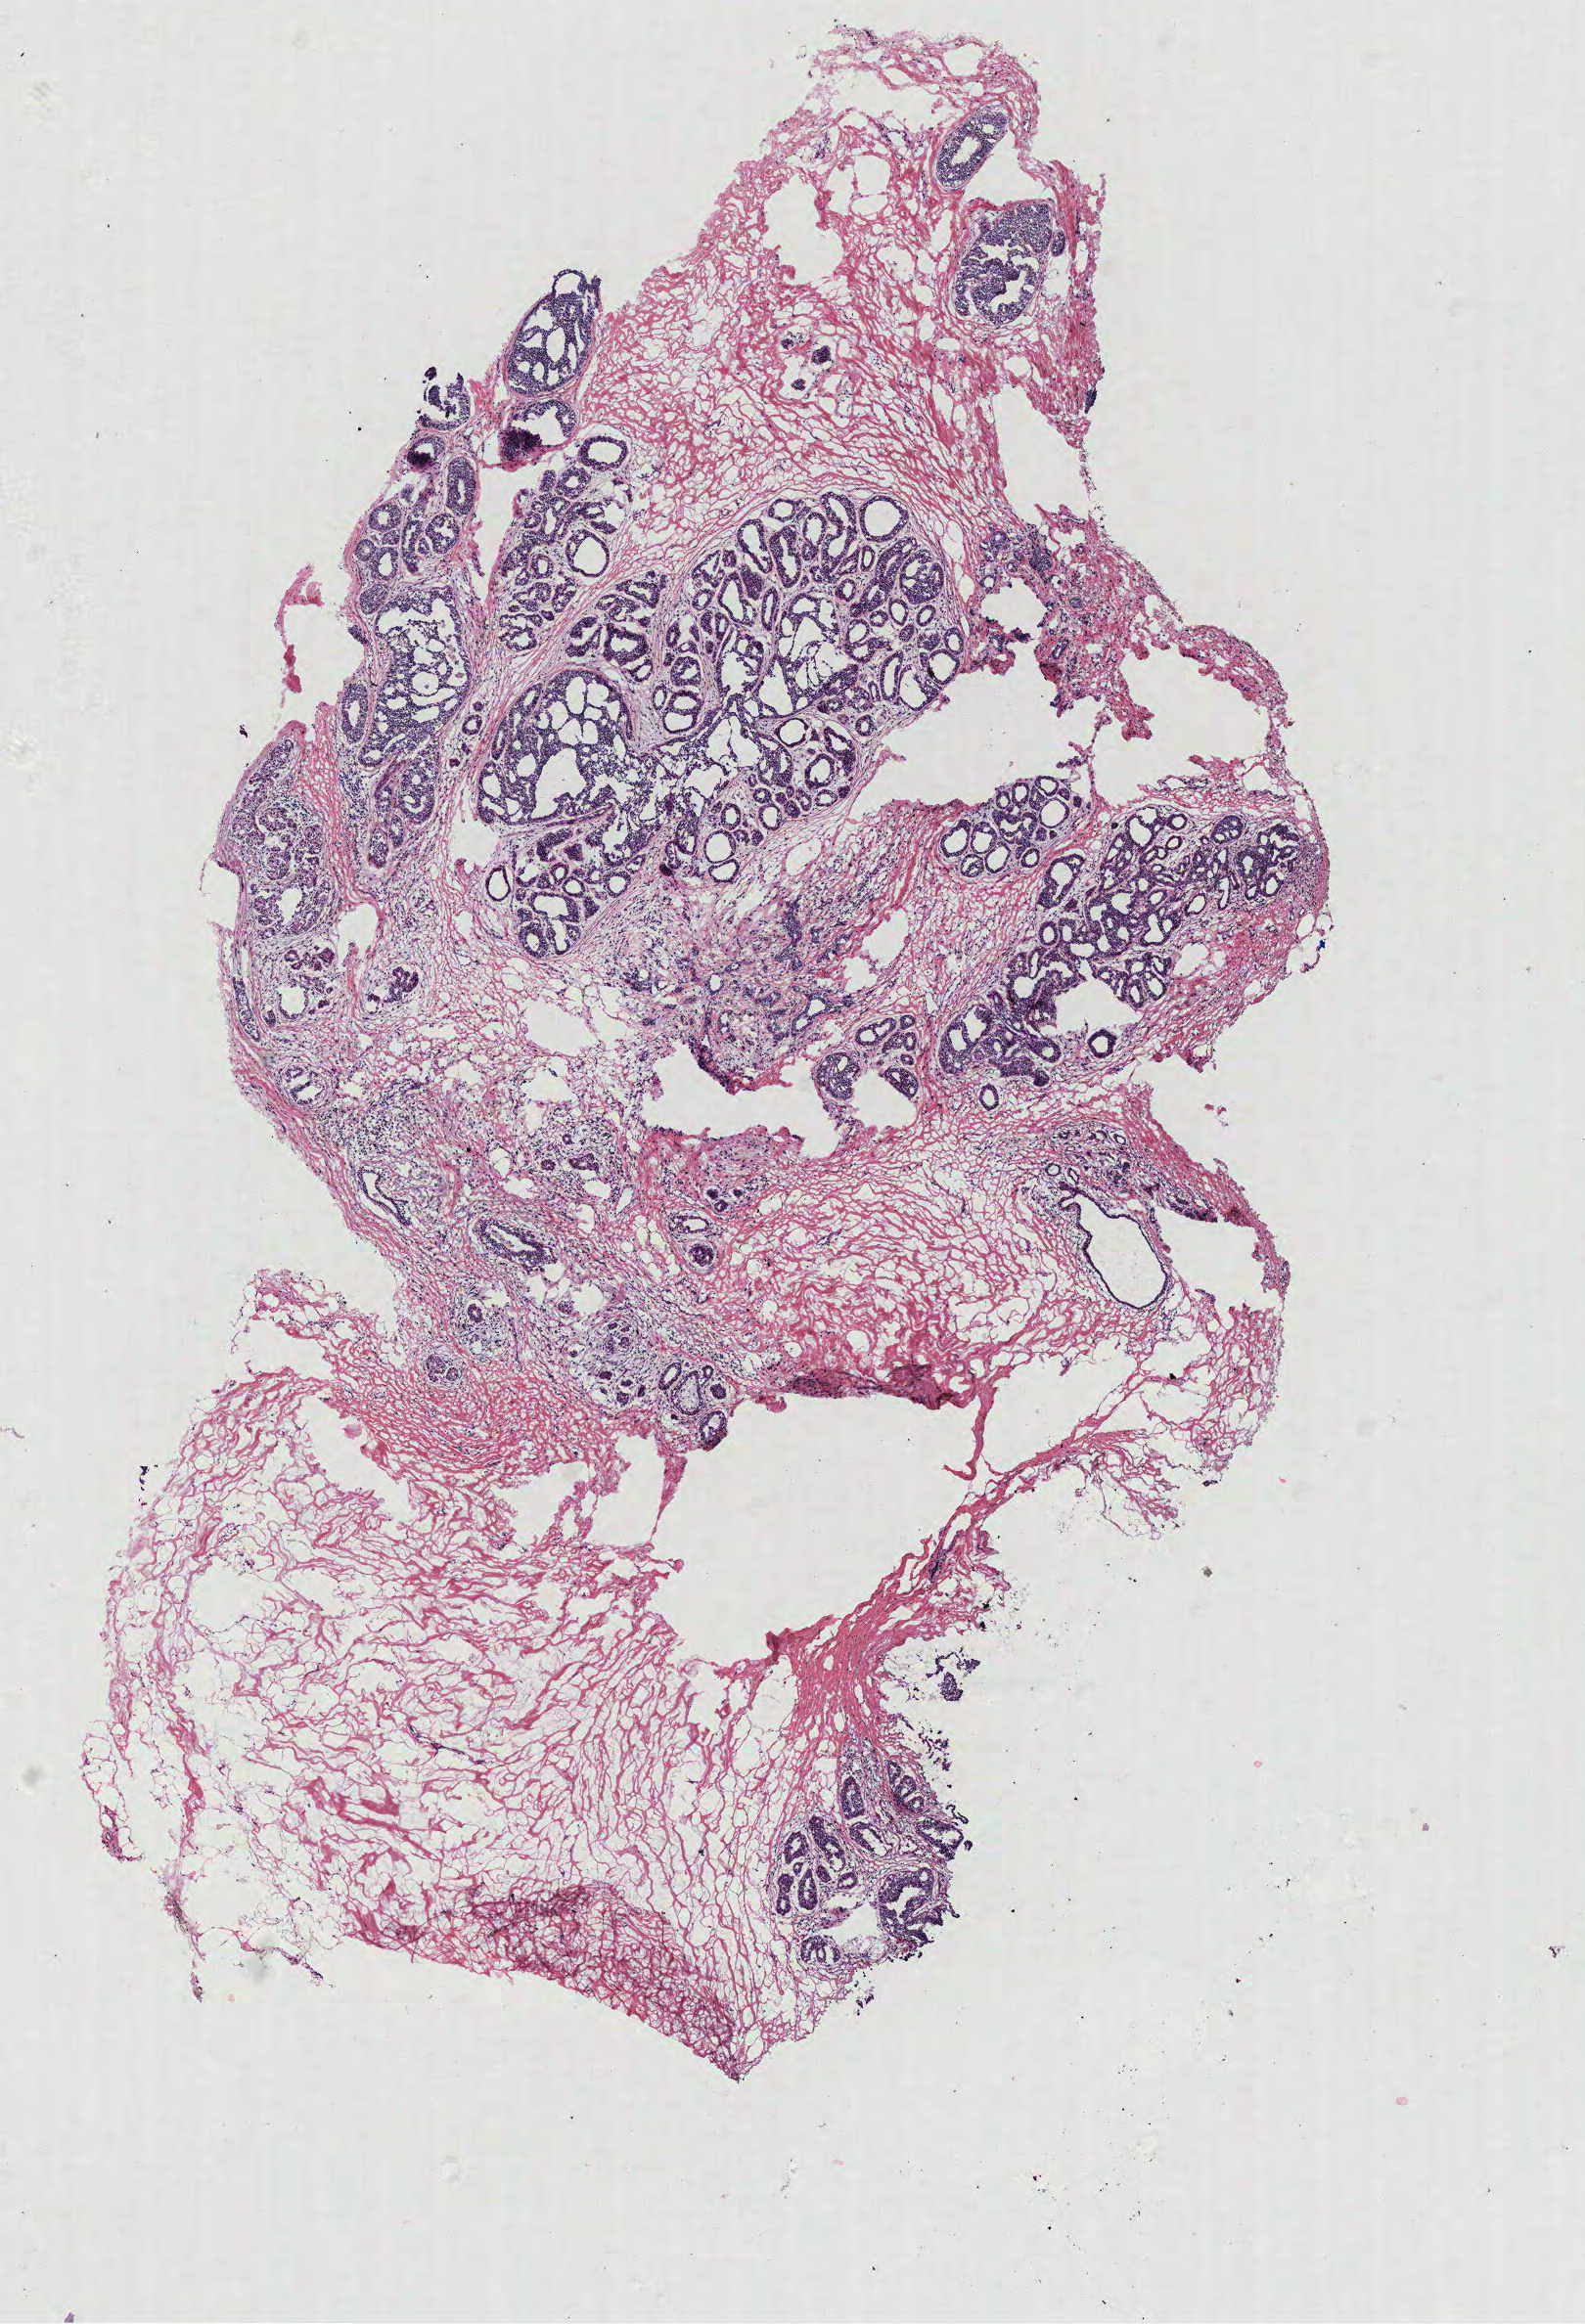
Digitized H&E tissue section (whole slide), low-resolution overview of the scanned area, about 6.5 x 9.5 mm (acquisition: 40x scan). Breast, tissue type not recorded. Patient: female, age 46 years.
• patient diagnosis: Infiltrating duct carcinoma, NOS